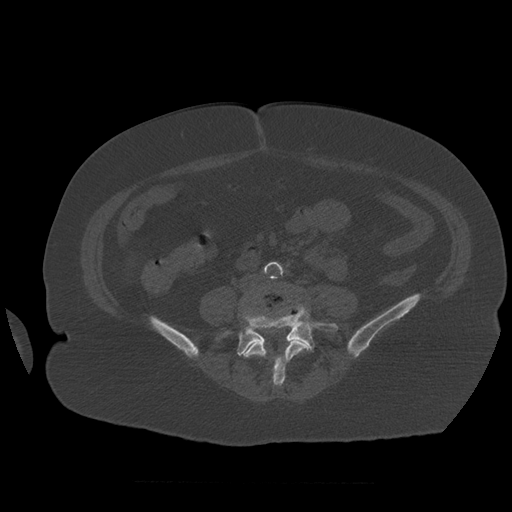
CT including the spine, one axial slice; slice 193 of 399 in the series (ordered by position); bone window (W 1800 / L 400 HU); 1.25 mm slice thickness; 512 × 512 image matrix, field of view 404 × 404 mm. Patient age 81 years. From the clinical record (not read from this slice): primary cancer: renal.
Annotated regions visible in this slice (semi-automatic segmentation, software-assisted and operator-edited):
- L4 vertebra: bounding box [x1, y1, x2, y2] px = [244, 336, 310, 387]
- L5 vertebra: [219, 305, 339, 357]